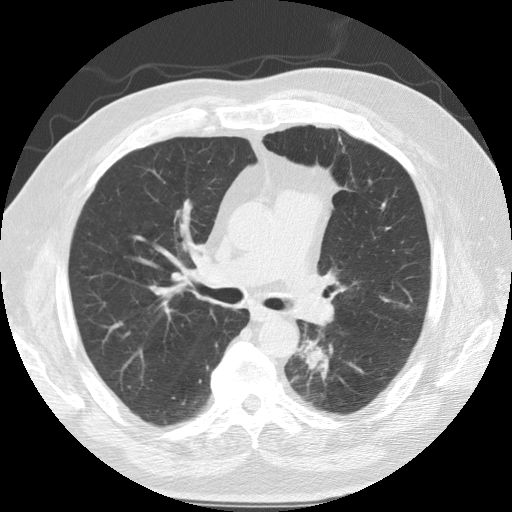
Low-dose screening chest CT, axial slice. First (baseline) screen. Lung window (W 1500 / L -600 HU). 2.5 mm slice thickness. Slice 52 of 124 in the series. Male participant, aged 68 years at enrolment. Former smoker at enrolment.
• Expert-annotated lung lesion, bounding box [x1, y1, x2, y2] px = [280, 318, 352, 397].
• The screening reader recorded 3 non-calcified nodules or masses ≥4 mm on this exam (left lower lobe, lingula, right lower lobe); which of them this box marks is not recorded.
• Official screen result: positive, change unspecified: nodule(s) >= 4 mm or enlarging nodule(s), mass(es), or other non-specific abnormalities suspicious for lung cancer.